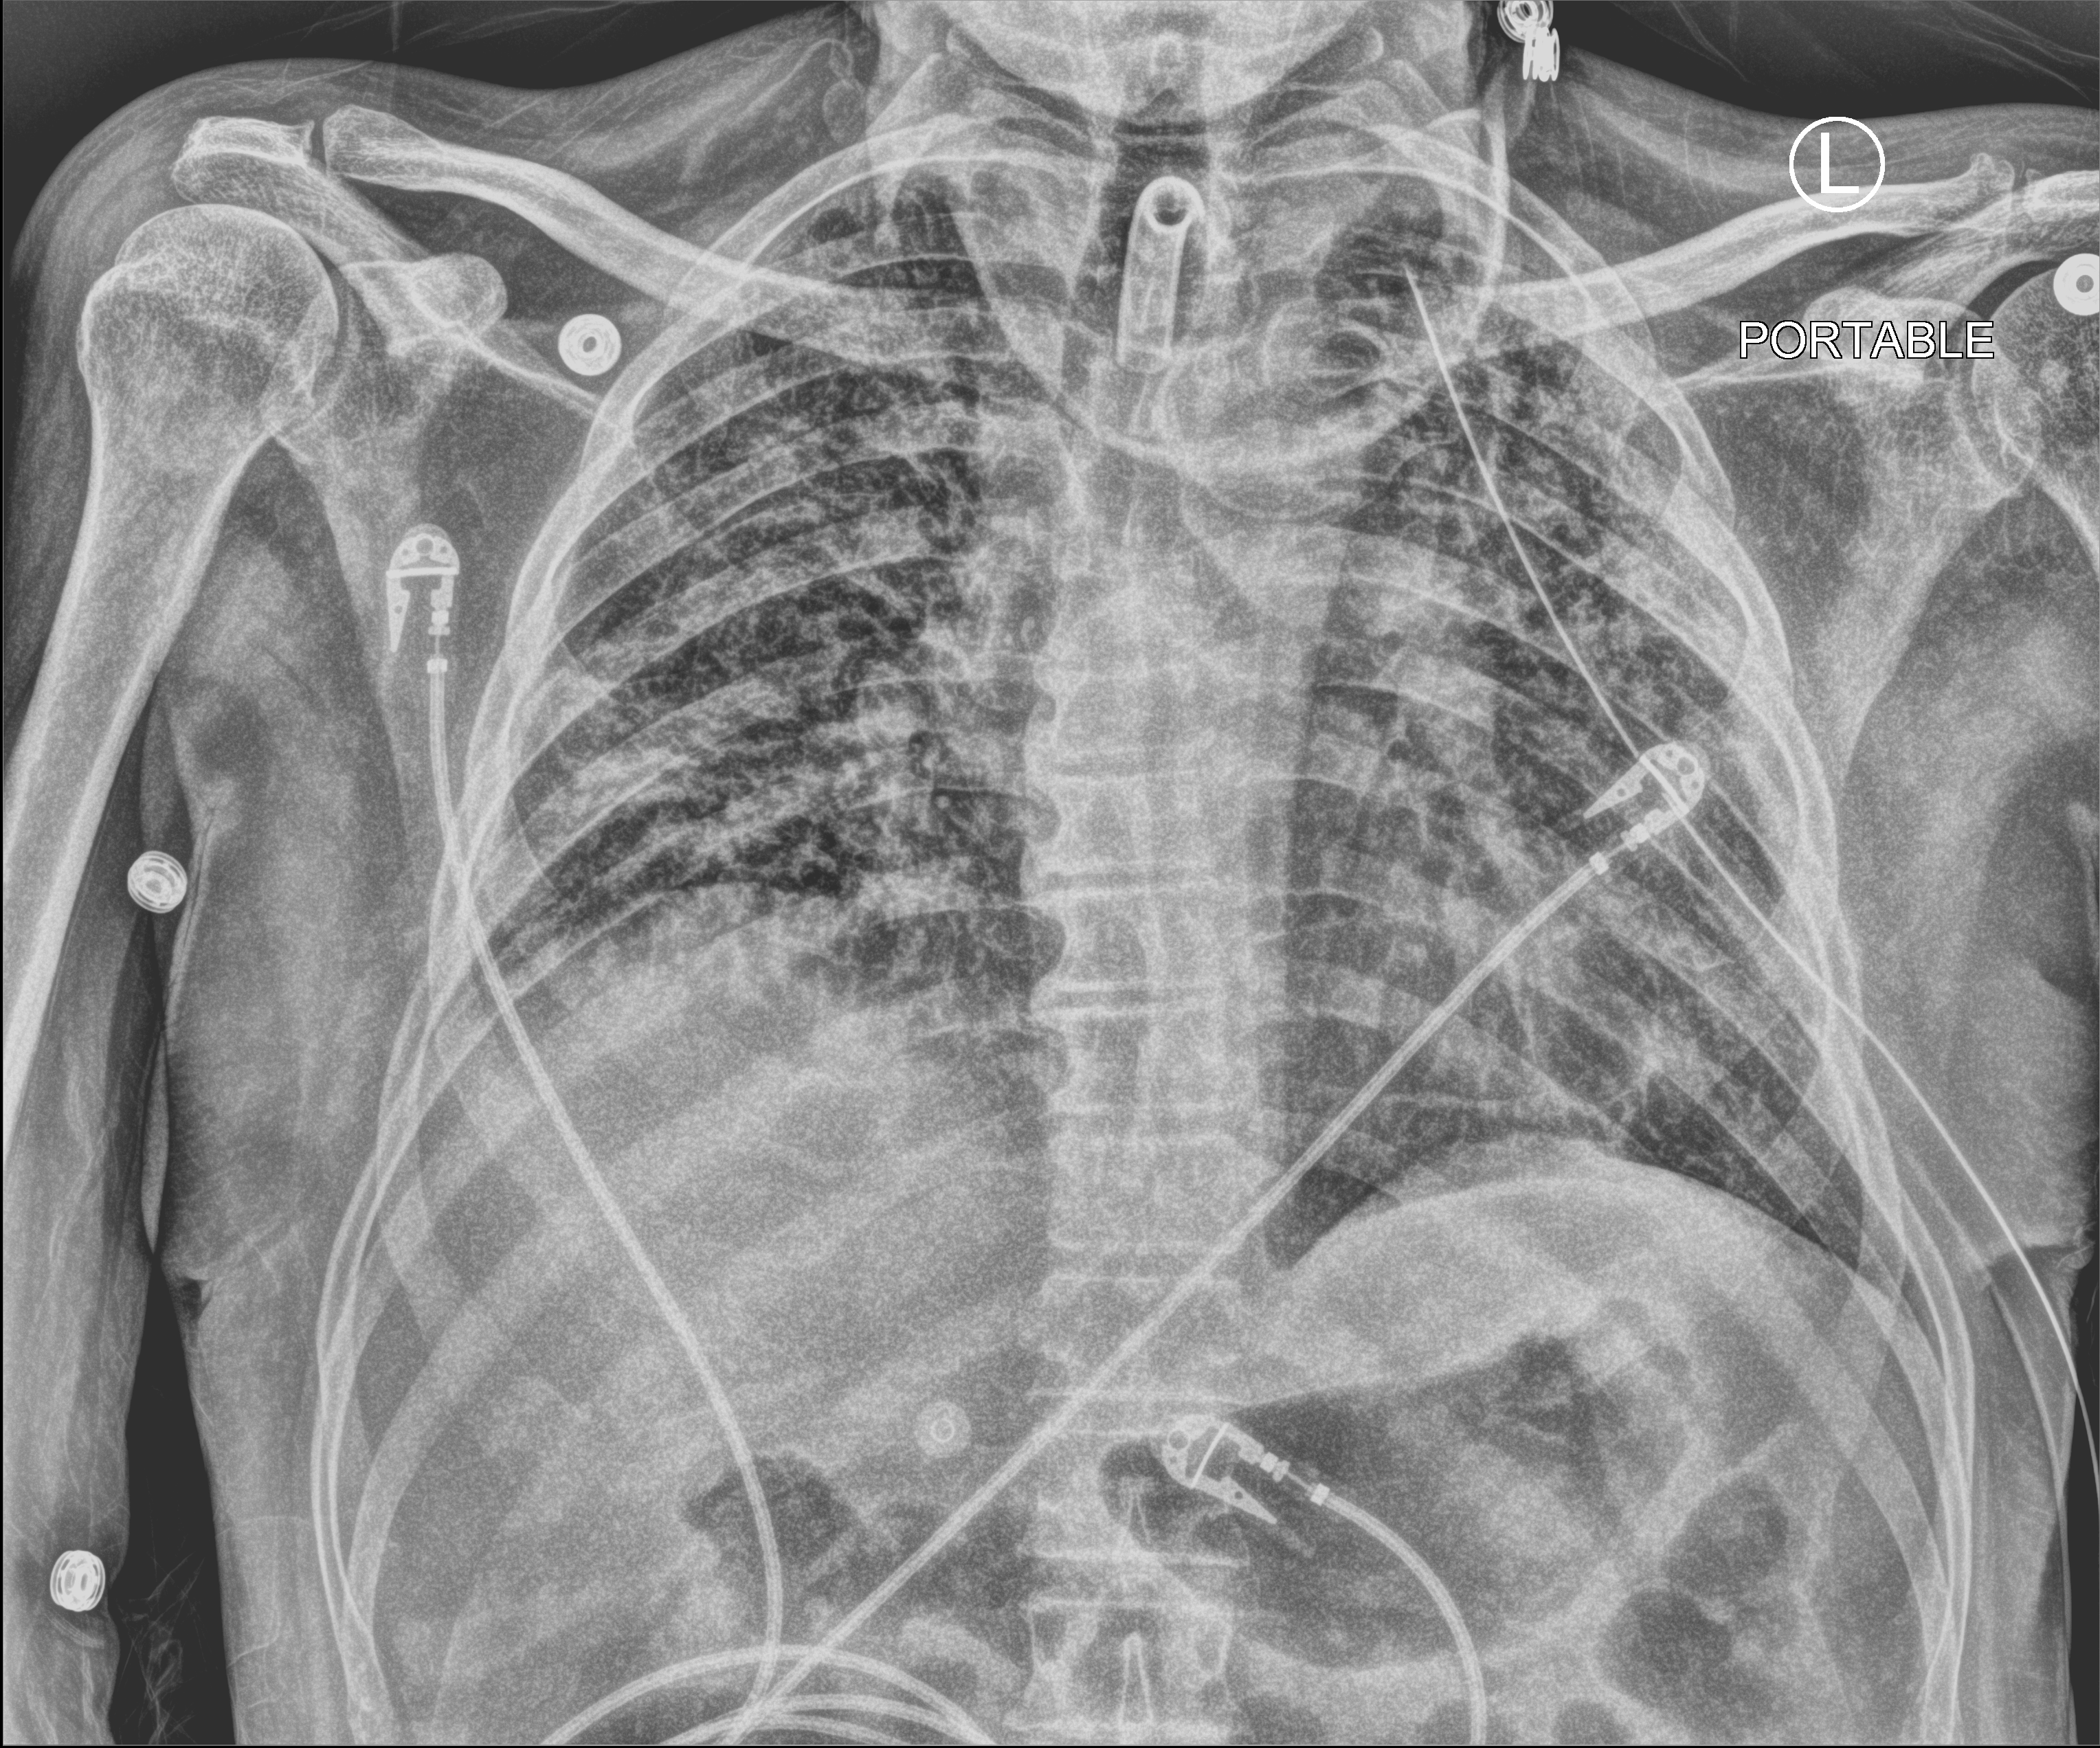
Portable chest radiograph, anteroposterior (AP) projection. Patient hospitalised with COVID-19; male, aged 18–59 years.
Admission-level facts for this patient (not findings on this image; timing relative to this image not recorded): admitted to intensive care during this hospital stay: yes; mechanically ventilated during this hospital stay: yes.